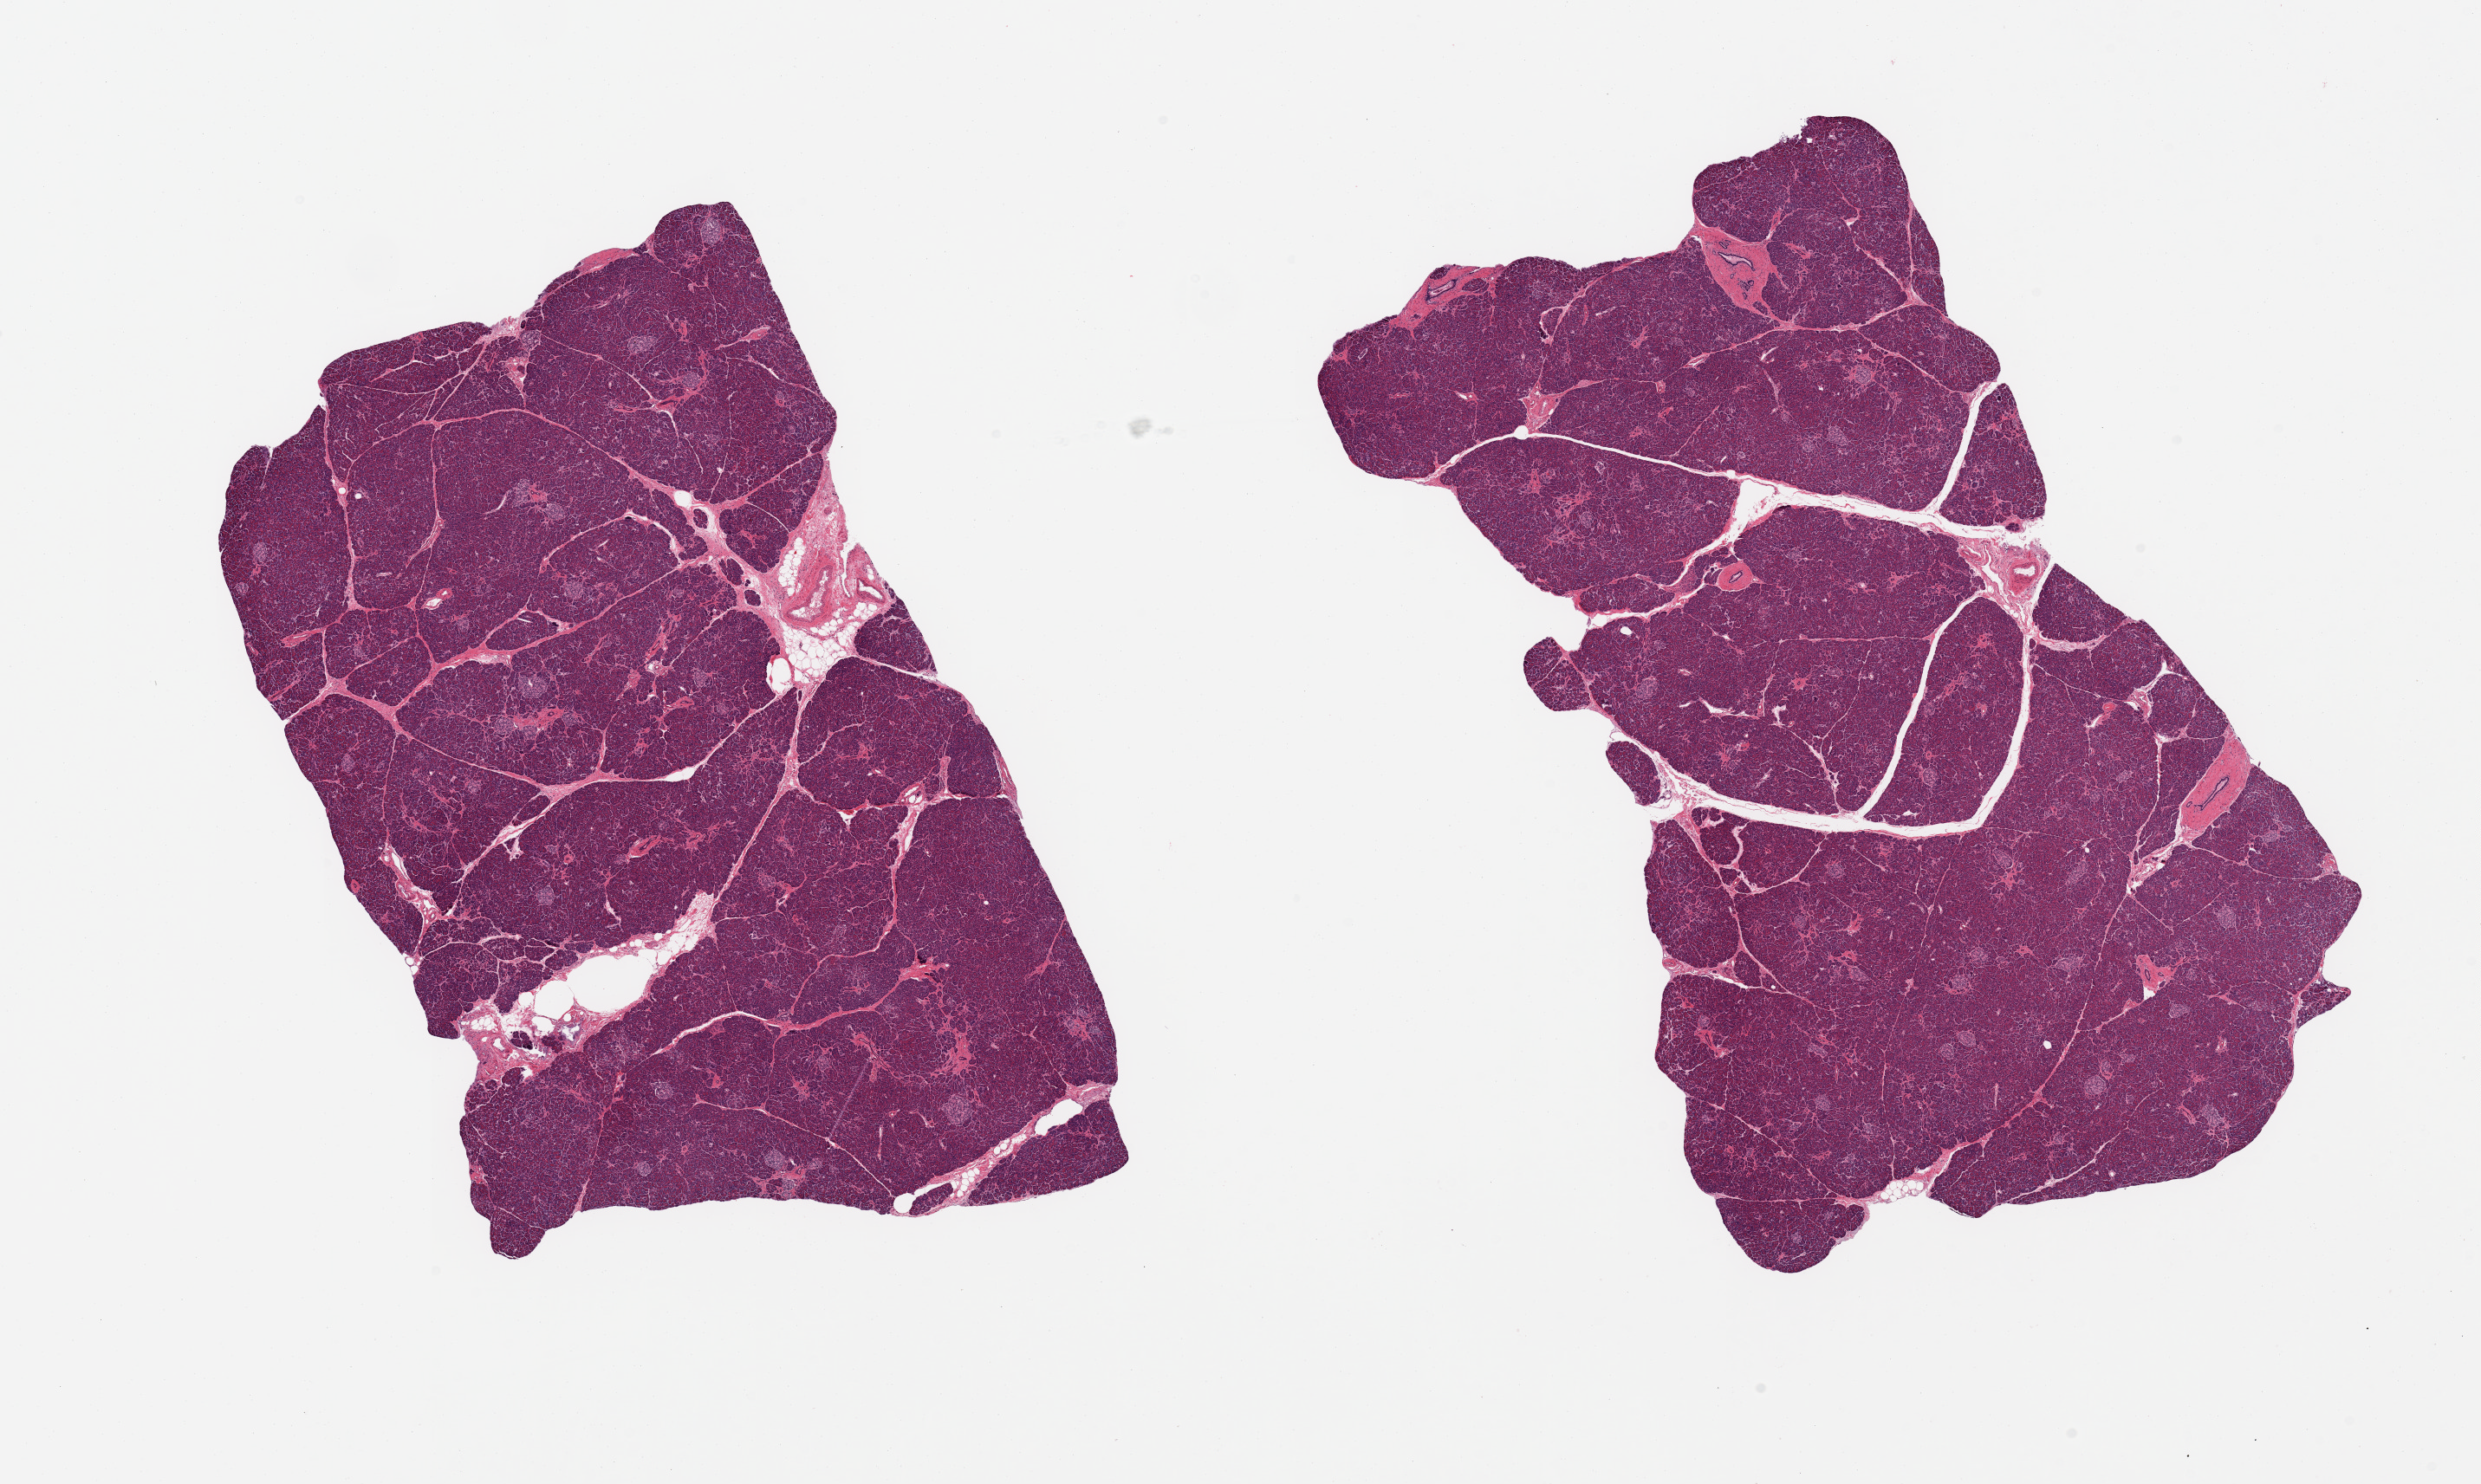
Hematoxylin and eosin (H&E) whole-slide image, brightfield, a low-resolution overview of the entire scanned area, about 22.6 x 13.5 mm. PAXgene-fixed paraffin-embedded (PFPE) section. Target tissue: pancreas. Tissue donor sample. Donor: female.
Review note (as recorded): 2 pieces; well preserved, numerous islets seen.